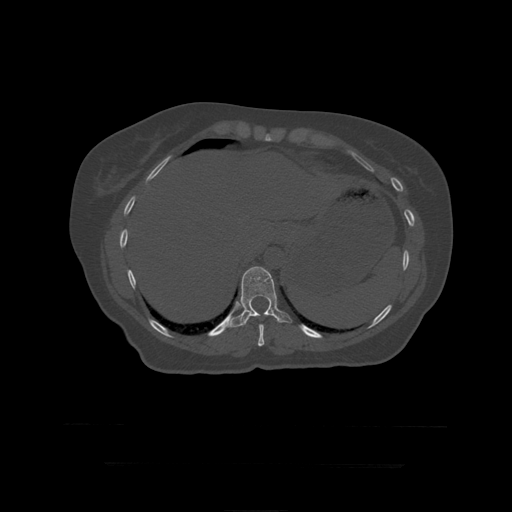
CT including the spine, one axial slice. Slice 226 of 399 in the series (ordered by position). Reconstruction kernel STANDARD. 120 kVp. Bone window (W 1800 / L 400 HU). 1.25 mm slice thickness. 512 × 512 image matrix. Patient age 41 years. Case-level facts recorded for this patient, not image findings: primary cancer: breast.
Annotated regions visible in this slice (semi-automatically segmented with operator editing):
- T10 vertebra: box from (x=258, y=324) to (x=265, y=347) px
- T11 vertebra: (x=226, y=267)–(x=292, y=329)